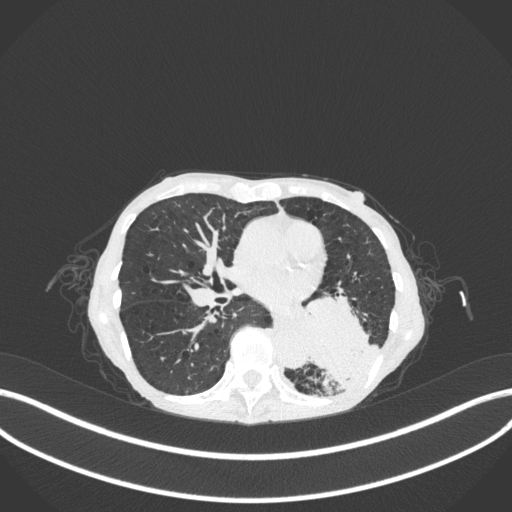
Chest CT, one axial slice. 120 kVp. Lung window (W 1500 / L -600 HU). 1 mm slice thickness. 512 × 512 image matrix, field of view 400 × 400 mm. Patient: female, 70 years. From the clinical record (not read from this slice): clinical TNM (as recorded): T3 N0 M0; histopathological grade: G3.
Outlined on this slice (bounding box drawn by a radiologist):
- lung tumour (recorded histology: small cell carcinoma): box from (x=291, y=289) to (x=376, y=389) px